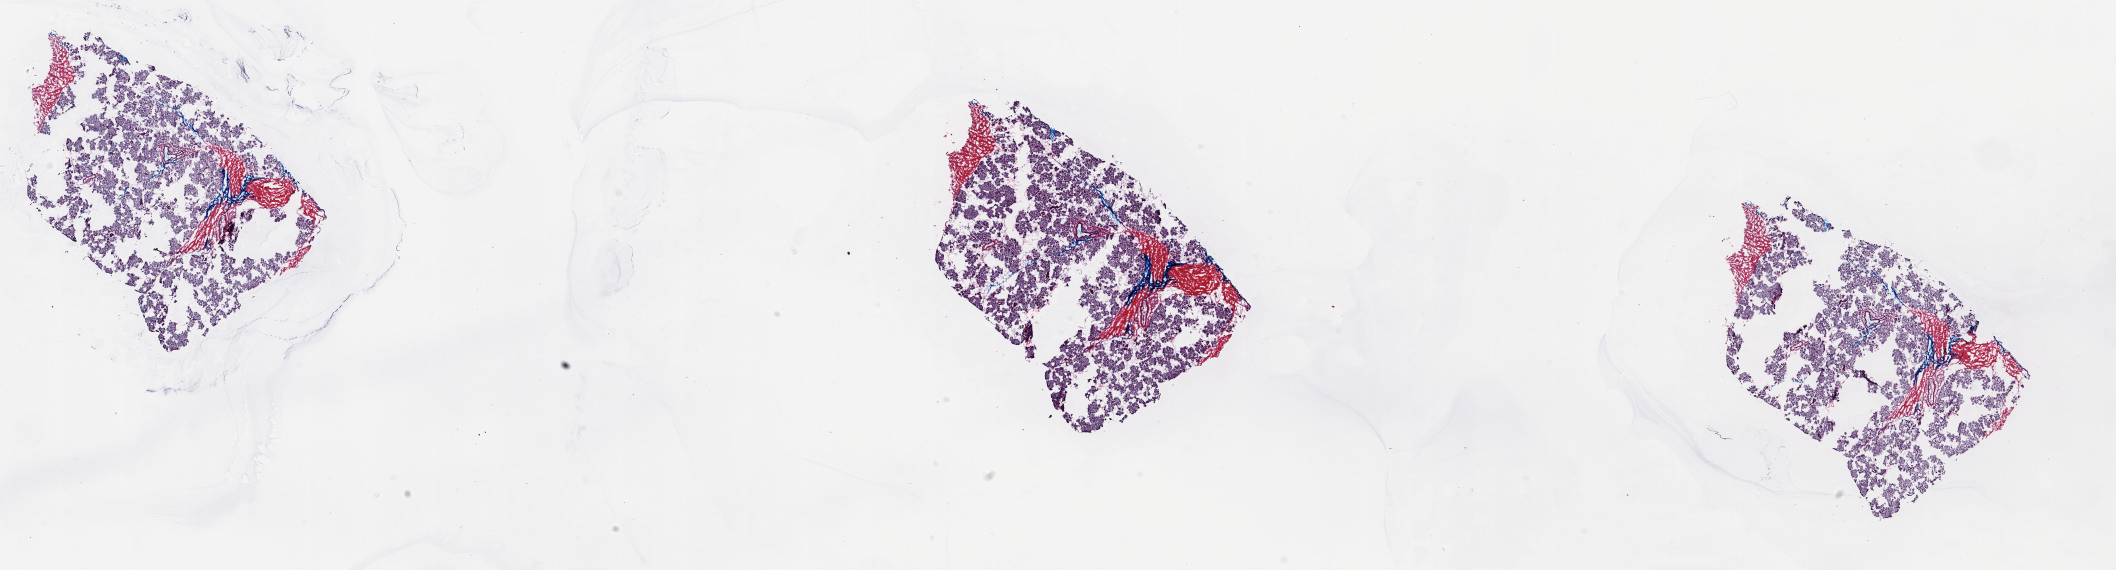
H&E whole-slide image, a low-resolution overview of the entire scanned area, about 33.4 x 9.0 mm (acquisition: 20x scan), frozen section from the top of the tissue portion, skin, solid tissue normal (non-tumour tissue) sample. Patient: male, age at initial diagnosis 68 years. Slide review estimates, as recorded: tumour cells 0%, tumour nuclei 0%, normal cells 100%, stromal cells 0%, necrosis 0%. Infiltration values recorded for this section: lymphocyte infiltration 0%, monocyte infiltration 0%, neutrophil infiltration 0%.
This section: solid tissue normal sample (biorepository sample class). Patient diagnosis: Malignant melanoma, NOS.